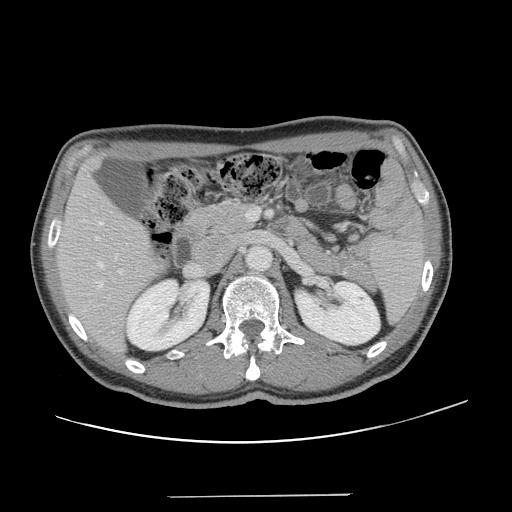
Contrast-enhanced abdominal CT, one axial slice. 120 kVp. Soft-tissue window (W 400 / L 40 HU). 2.5 mm slice thickness. 512 × 512 image matrix, field of view 403 × 403 mm. Male patient, age 60 years. From the clinical record (not read from this slice): diagnosis: colorectal cancer liver metastases, imaged before liver resection; multiple liver metastases: no; largest metastasis: 2.5 cm; disease in both lobes: no.
Outlined on this slice (outlined manually by an expert reader):
- hepatic veins: bounding box <98,222,103,288> (left, top, right, bottom; pixels)
- liver: <58,161,162,351>
- planned liver remnant (the part of the liver to remain after resection): <58,161,162,351>